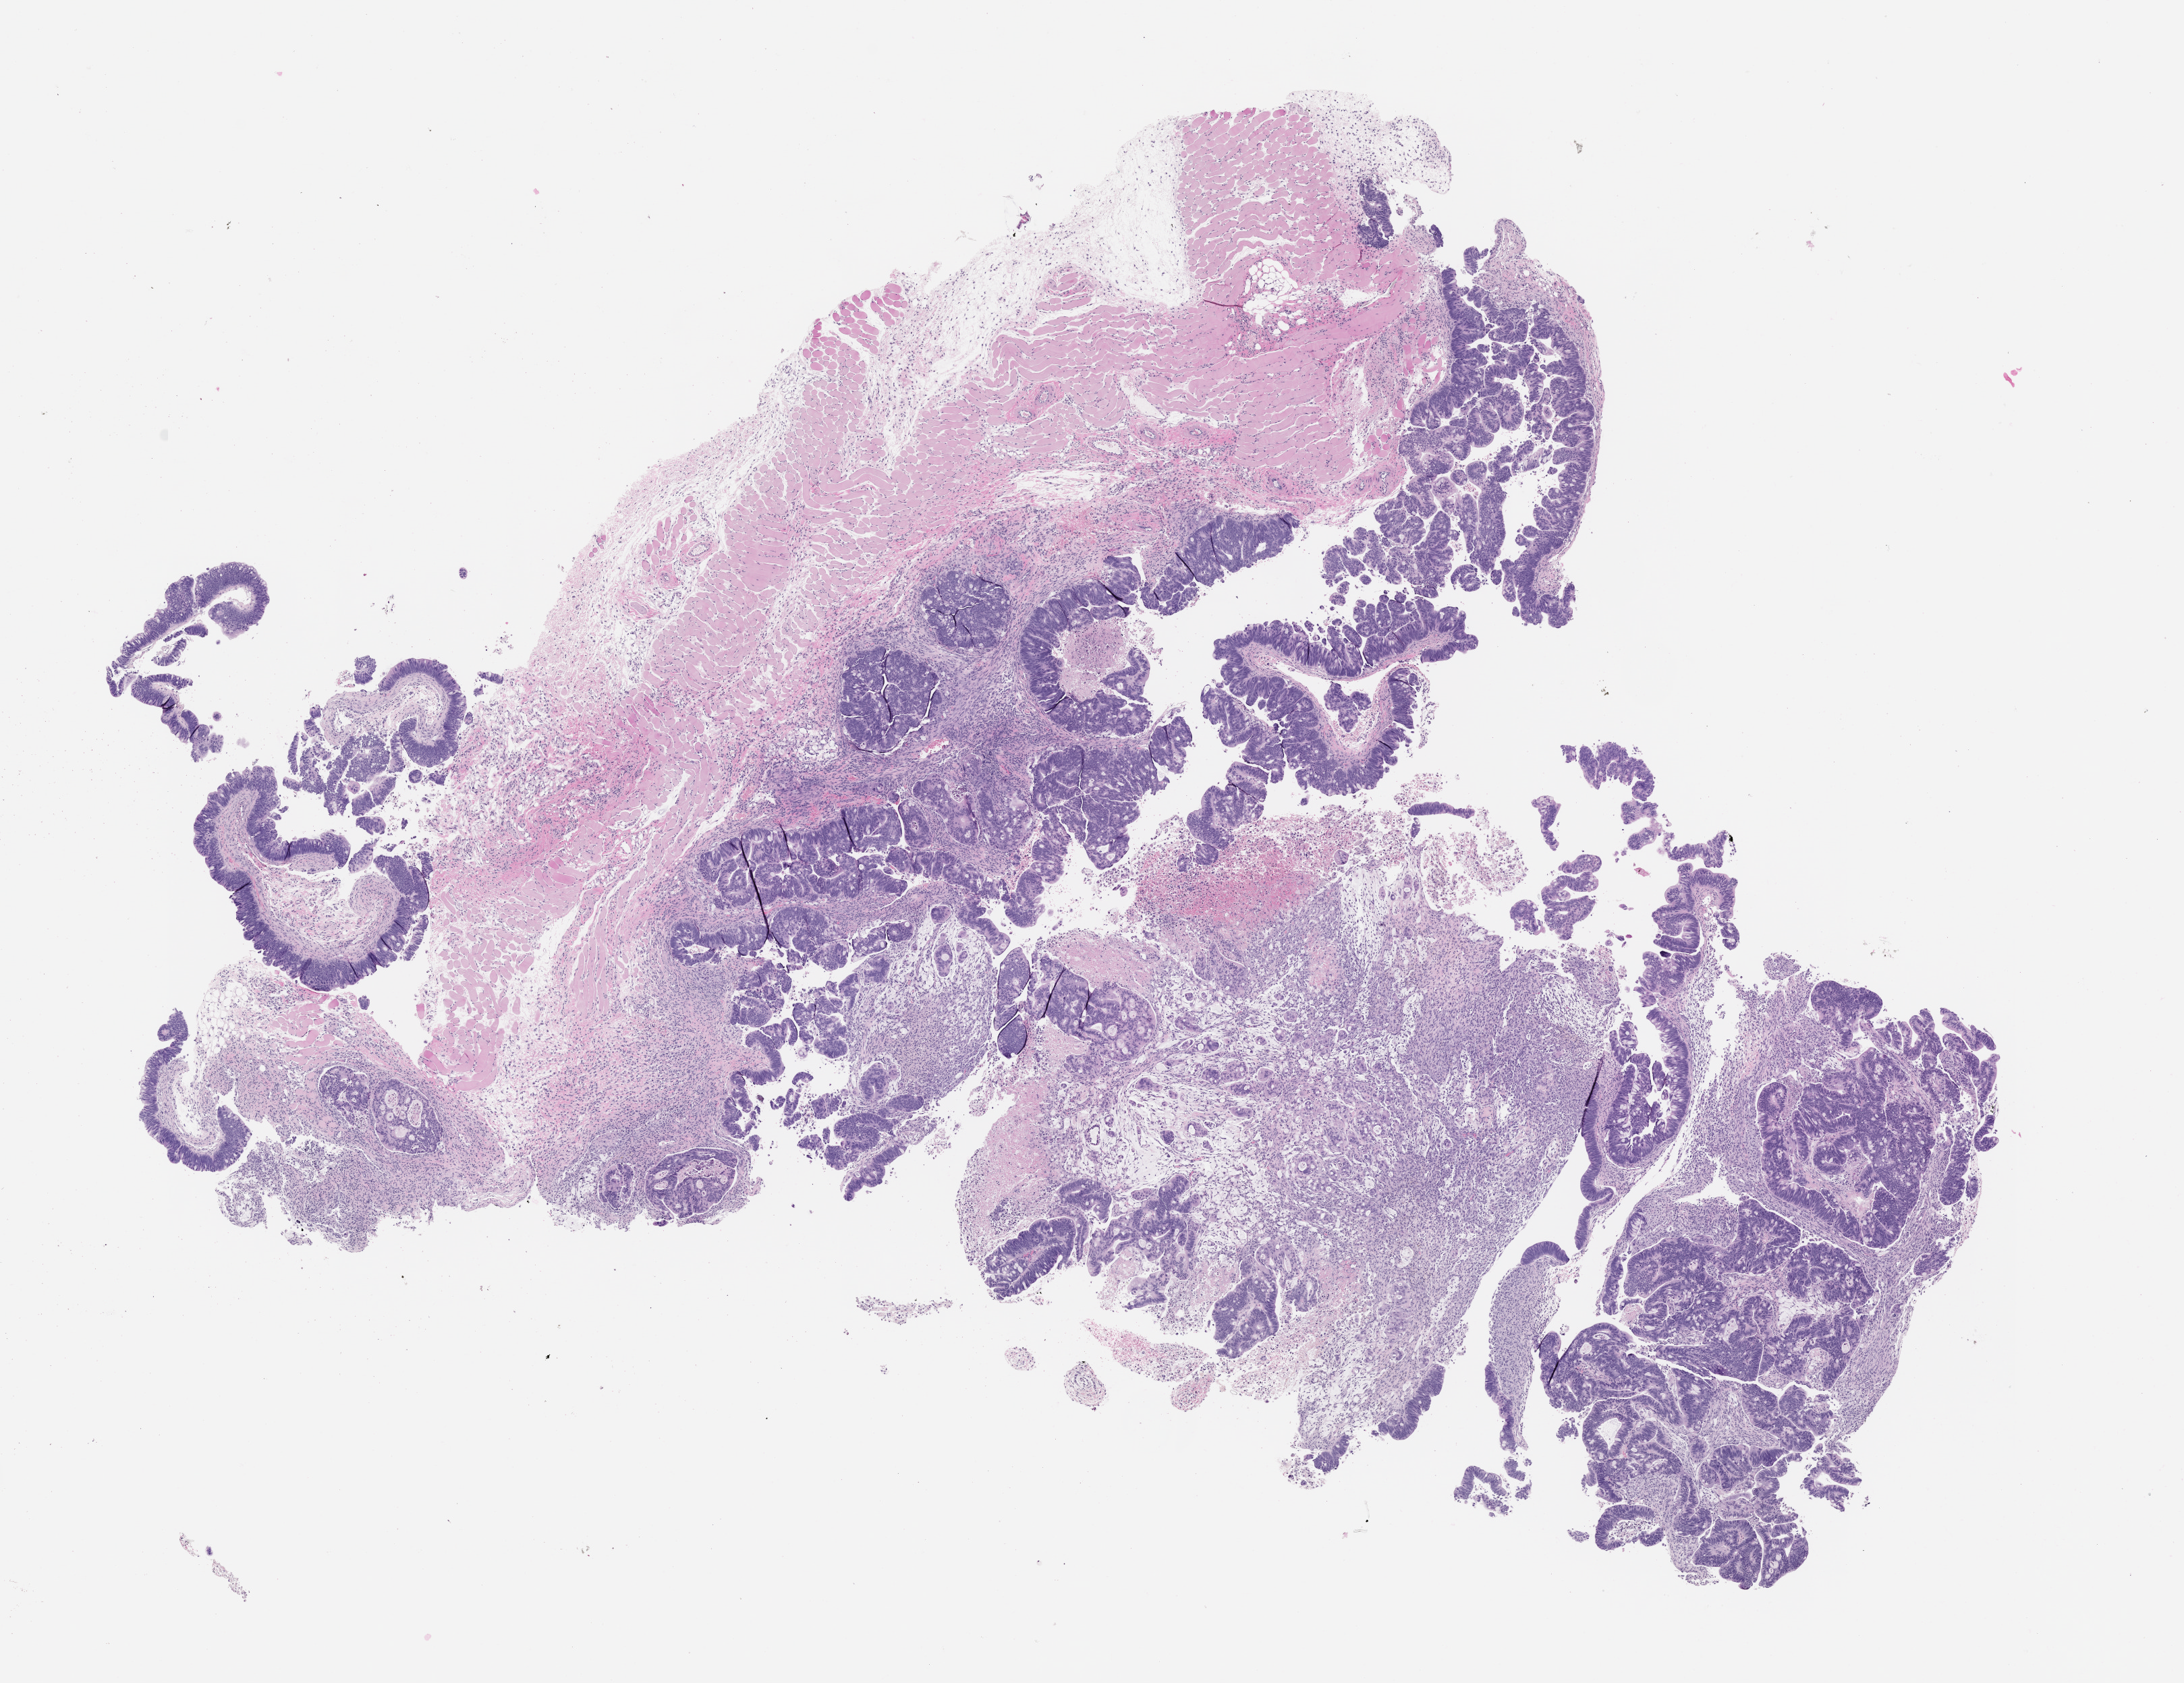
Whole-slide image, hematoxylin and eosin (H&E): patient-derived xenograft (human tumor grown in a mouse) — a low-resolution overview of the entire scanned area, about 13.0 x 10.0 mm, formalin-fixed, paraffin-embedded (FFPE) tissue, tumor site category: colon.
Originating patient diagnosis: Colon Adenocarcinoma.